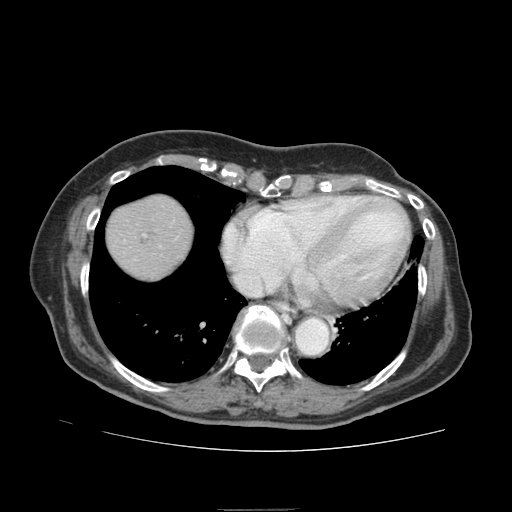
Contrast-enhanced abdominal CT (liver protocol), one axial slice. Slice 78 of 95 in the series (ordered by position). Reconstruction kernel STANDARD. 140 kVp. Soft-tissue window (W 400 / L 40 HU). 2.5 mm slice thickness. 512 × 512 image matrix, field of view 360 × 360 mm. From the clinical record (not read from this slice): diagnosis: hepatocellular carcinoma (patient treated with transarterial chemoembolisation; whether this scan precedes or follows treatment is not stated here); TNM stage (as recorded): Stage-IVA; Child-Pugh class: B; tumour nodularity: uninodular.
Outlined on this slice (semi-automatically segmented with operator editing):
- abdominal aorta: box from (x=296, y=318) to (x=327, y=353) px
- liver parenchyma outside the tumour (the mass and vessels are separate outlines, so this box may not span the whole liver): (x=106, y=194)–(x=192, y=279)